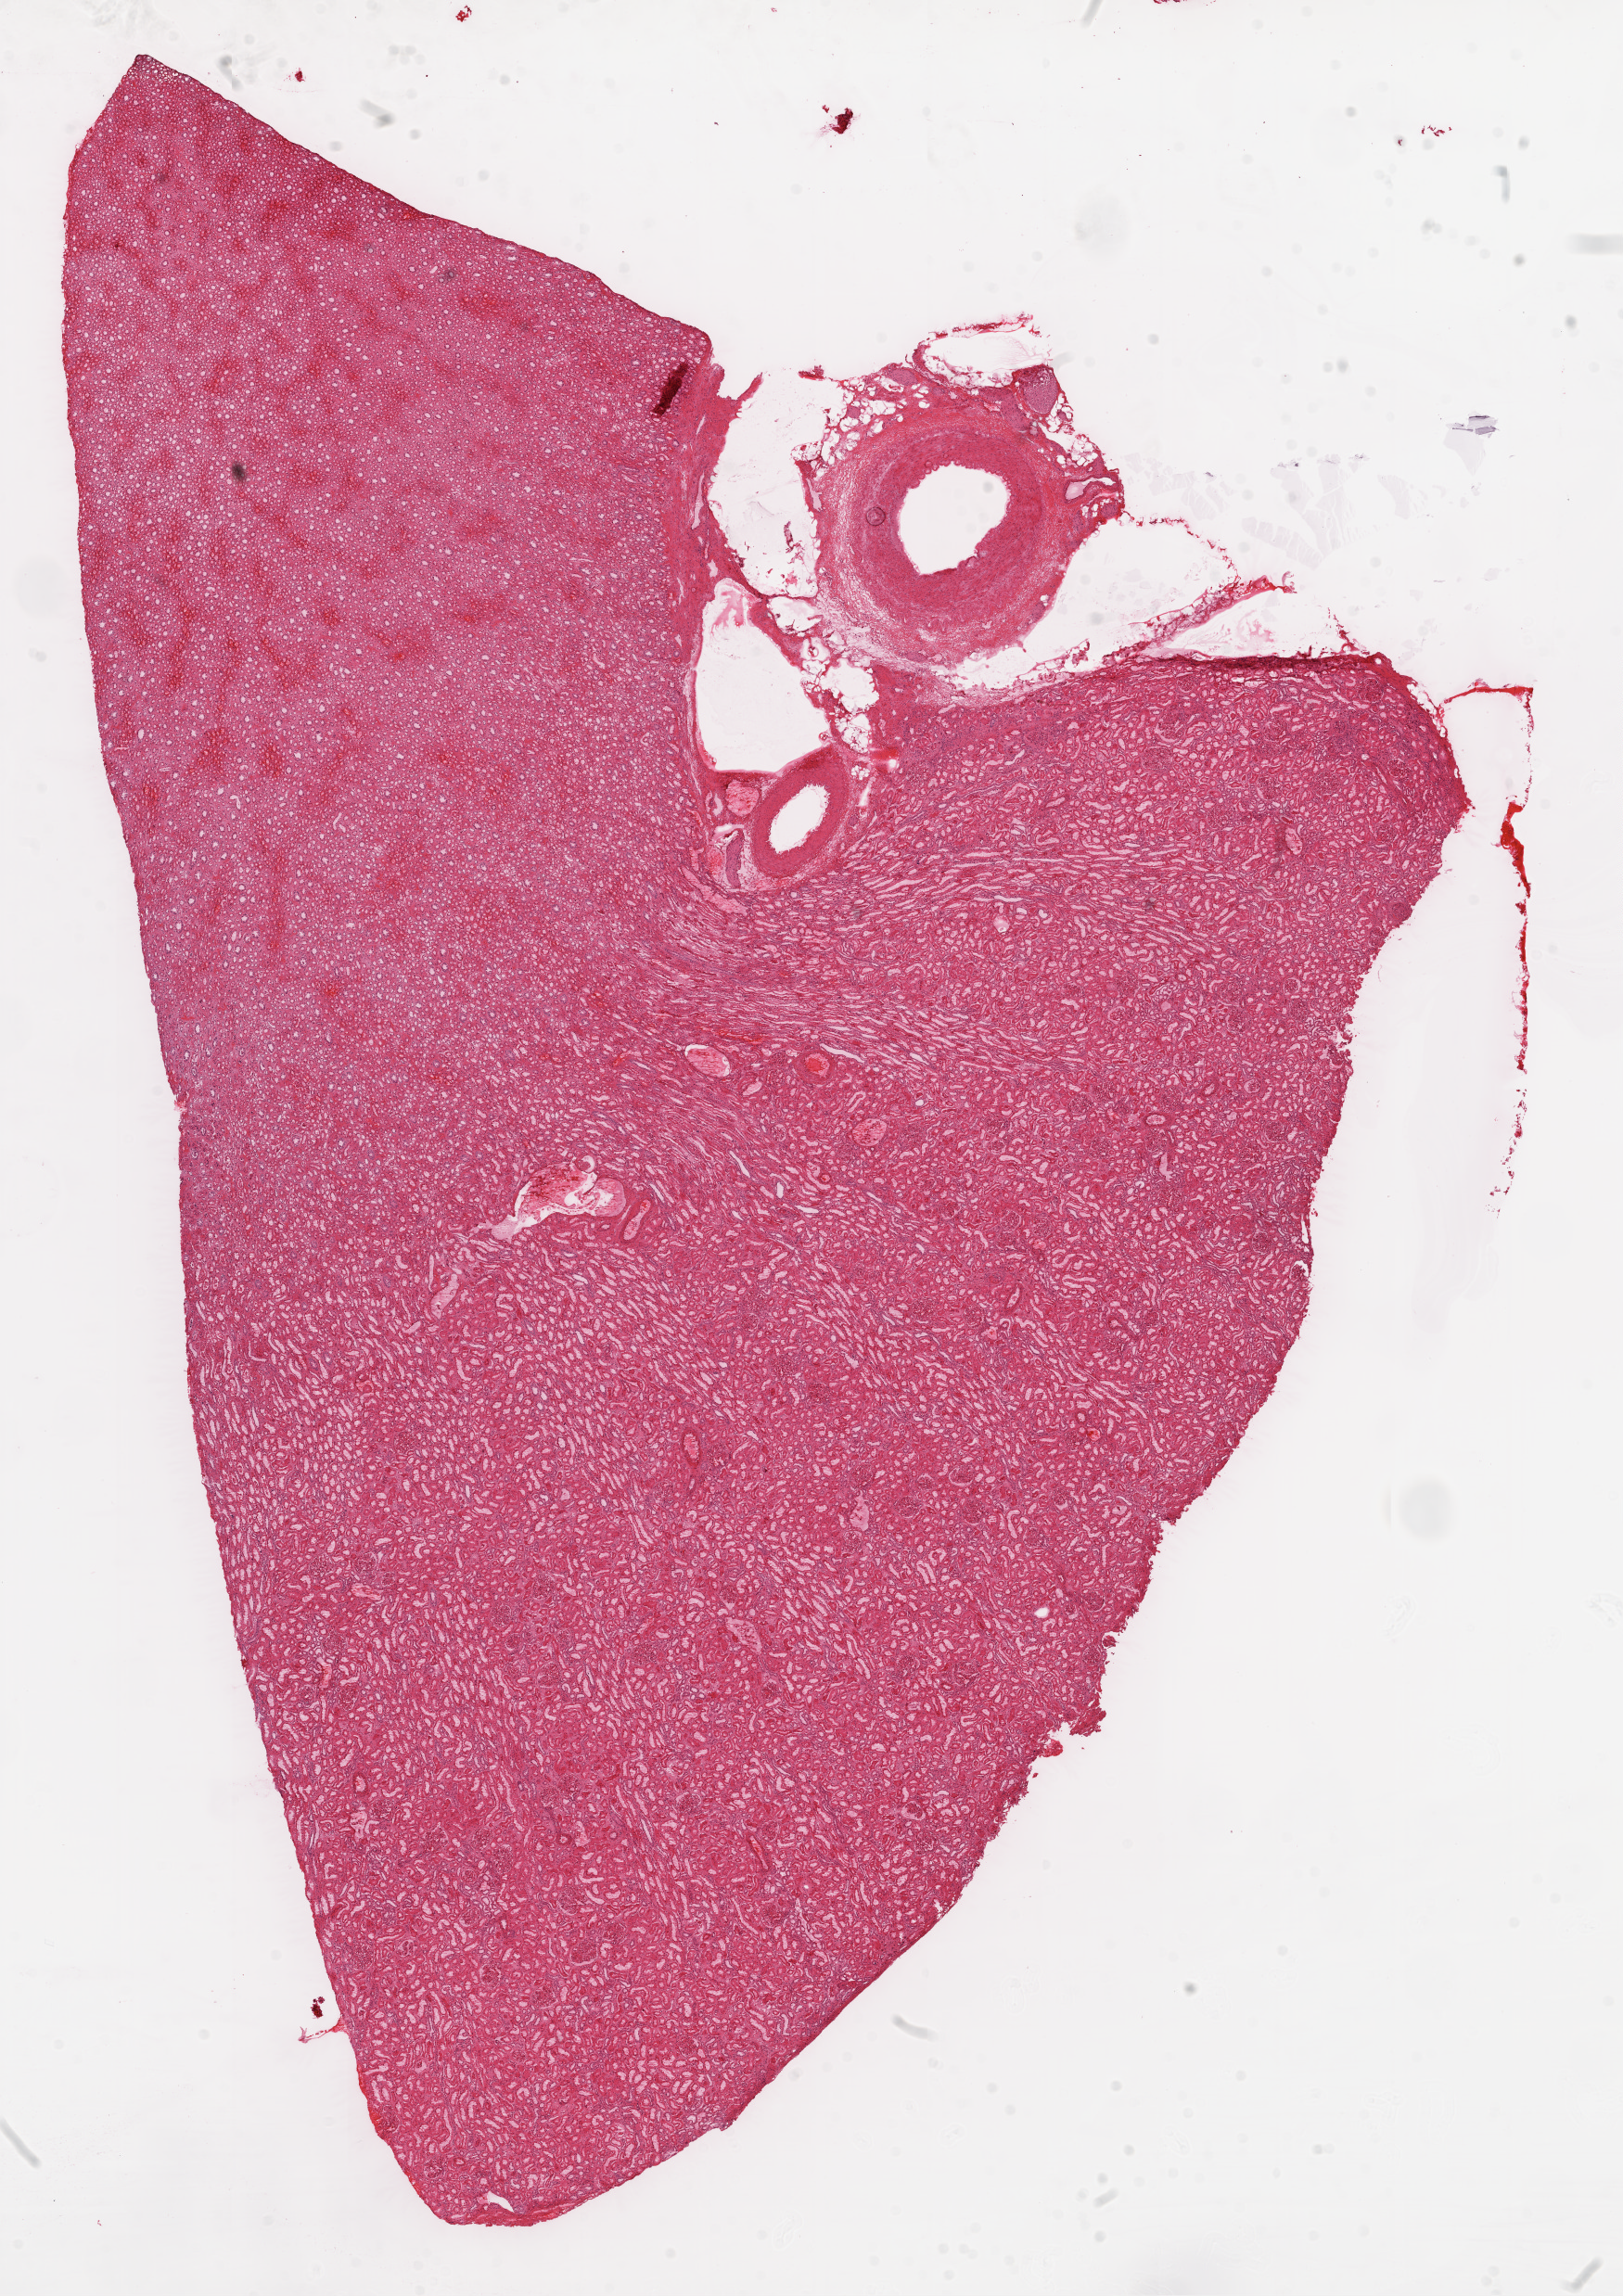
H&E-stained whole-slide image, low-resolution overview of the scanned area, about 14.0 x 19.9 mm. Frozen section from the top of the tissue portion. Solid tissue normal (non-tumour tissue) sample from the kidney. Male patient; age at initial diagnosis 43 years.
This section: solid tissue normal sample (biorepository sample class). Patient diagnosis: Clear cell adenocarcinoma, NOS.